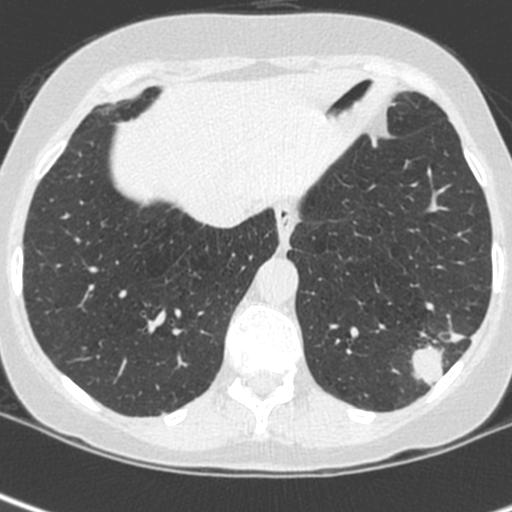
Axial slice from a low-dose chest CT screening exam; baseline screening round; lung window (W 1500 / L -600 HU); 1.3 mm slice thickness; standard (soft-tissue) reconstruction kernel (C); 512 × 512 image matrix, field of view 271 × 271 mm. Female, age 56 years at enrolment. Current smoker at enrolment.
Expert-annotated lung lesion, bounding box [x1, y1, x2, y2] px = [400, 303, 481, 386]. Screening reader's record for this exam (one nodule recorded; not confirmed to be the boxed lesion): non-calcified nodule or mass ≥4 mm, left lower lobe, 37 × 29 mm, spiculated (stellate) margins, ground glass attenuation. Participant outcome: lung cancer diagnosed 91 days after this screen — squamous cell carcinoma, NOS, left lower lobe, poorly differentiated (G3), stage IIIA (AJCC 6th edition), 35 mm at pathology.